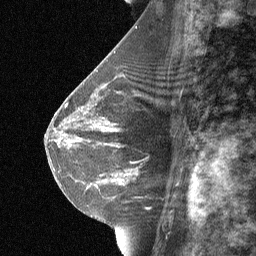
Breast MRI (dynamic contrast-enhanced), one sagittal slice; position 37 of 64 along the scan axis; dynamic contrast-enhanced study with each time point stored as its own series, time point 2 of 3 at this slice position (early post-contrast, ordered by acquisition time); 1.5 T; TE 4.8 ms, TR 27 ms; 2 mm slice thickness; 256 × 256 image matrix, field of view 180 × 180 mm. Female patient, age 42 years. From the clinical record (not read from this slice): setting: breast cancer imaged before/during neoadjuvant chemotherapy; receptor status: triple-negative.
Structures marked on this image (semi-automatic segmentation, software-assisted and operator-edited):
- analysis volume of interest (the breast-tissue region the enhancement analysis was run in; not a lesion): bounding box <99,117,174,187> (left, top, right, bottom; pixels)
- tumour enhancement mask (voxels above the 90 % enhancement threshold inside the analysis volume of interest): <125,168,138,176>